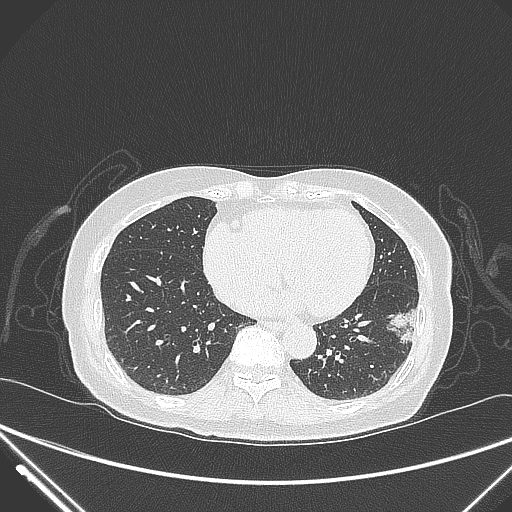
Chest CT, one axial slice. Slice 109 of 310 in the series (ordered by position). 120 kVp. Lung window (W 1500 / L -600 HU). 512 × 512 image matrix, field of view 377 × 377 mm. Female patient, age 82 years. Case-level facts recorded for this patient, not image findings: clinical TNM (as recorded): T1c N0 M0; histopathological grade: G2.
Outlined on this slice (bounding box drawn by a radiologist):
- lung tumour (recorded histology: adenocarcinoma): bounding box [x1, y1, x2, y2] px = [378, 296, 430, 356]